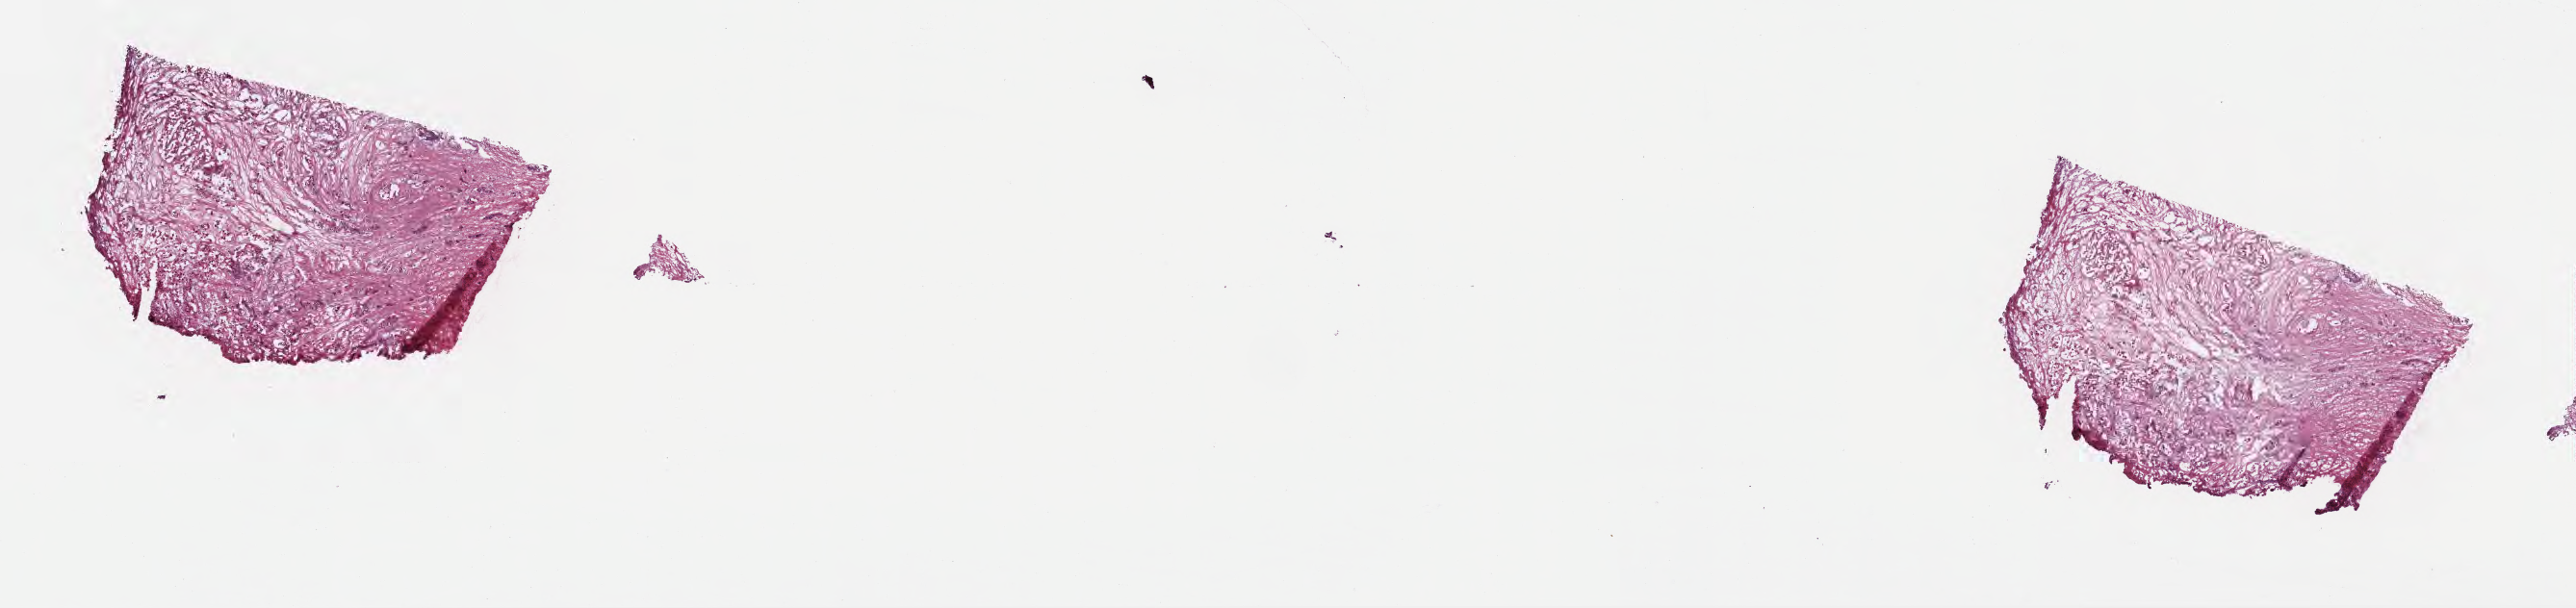
Hematoxylin and eosin (H&E) whole-slide image, low-resolution overview of the scanned area, about 21.6 x 5.1 mm; frozen section; specimen: primary tumor; anatomic site: head of pancreas. Patient: female, age at initial diagnosis 64 years. Tumor grade: G3 (poorly differentiated). Slide review estimates, as recorded: tumor cells 15%, tumor nuclei 80%, stromal cells 85%, necrosis 0%, normal cells 0%. Inflammatory infiltration, as recorded: lymphocyte infiltration 0%, monocyte infiltration 0%, neutrophil infiltration 0%.
* AJCC pathologic stage: Stage III
* section: top of the tissue portion
* histologic diagnosis: Infiltrating duct carcinoma, NOS